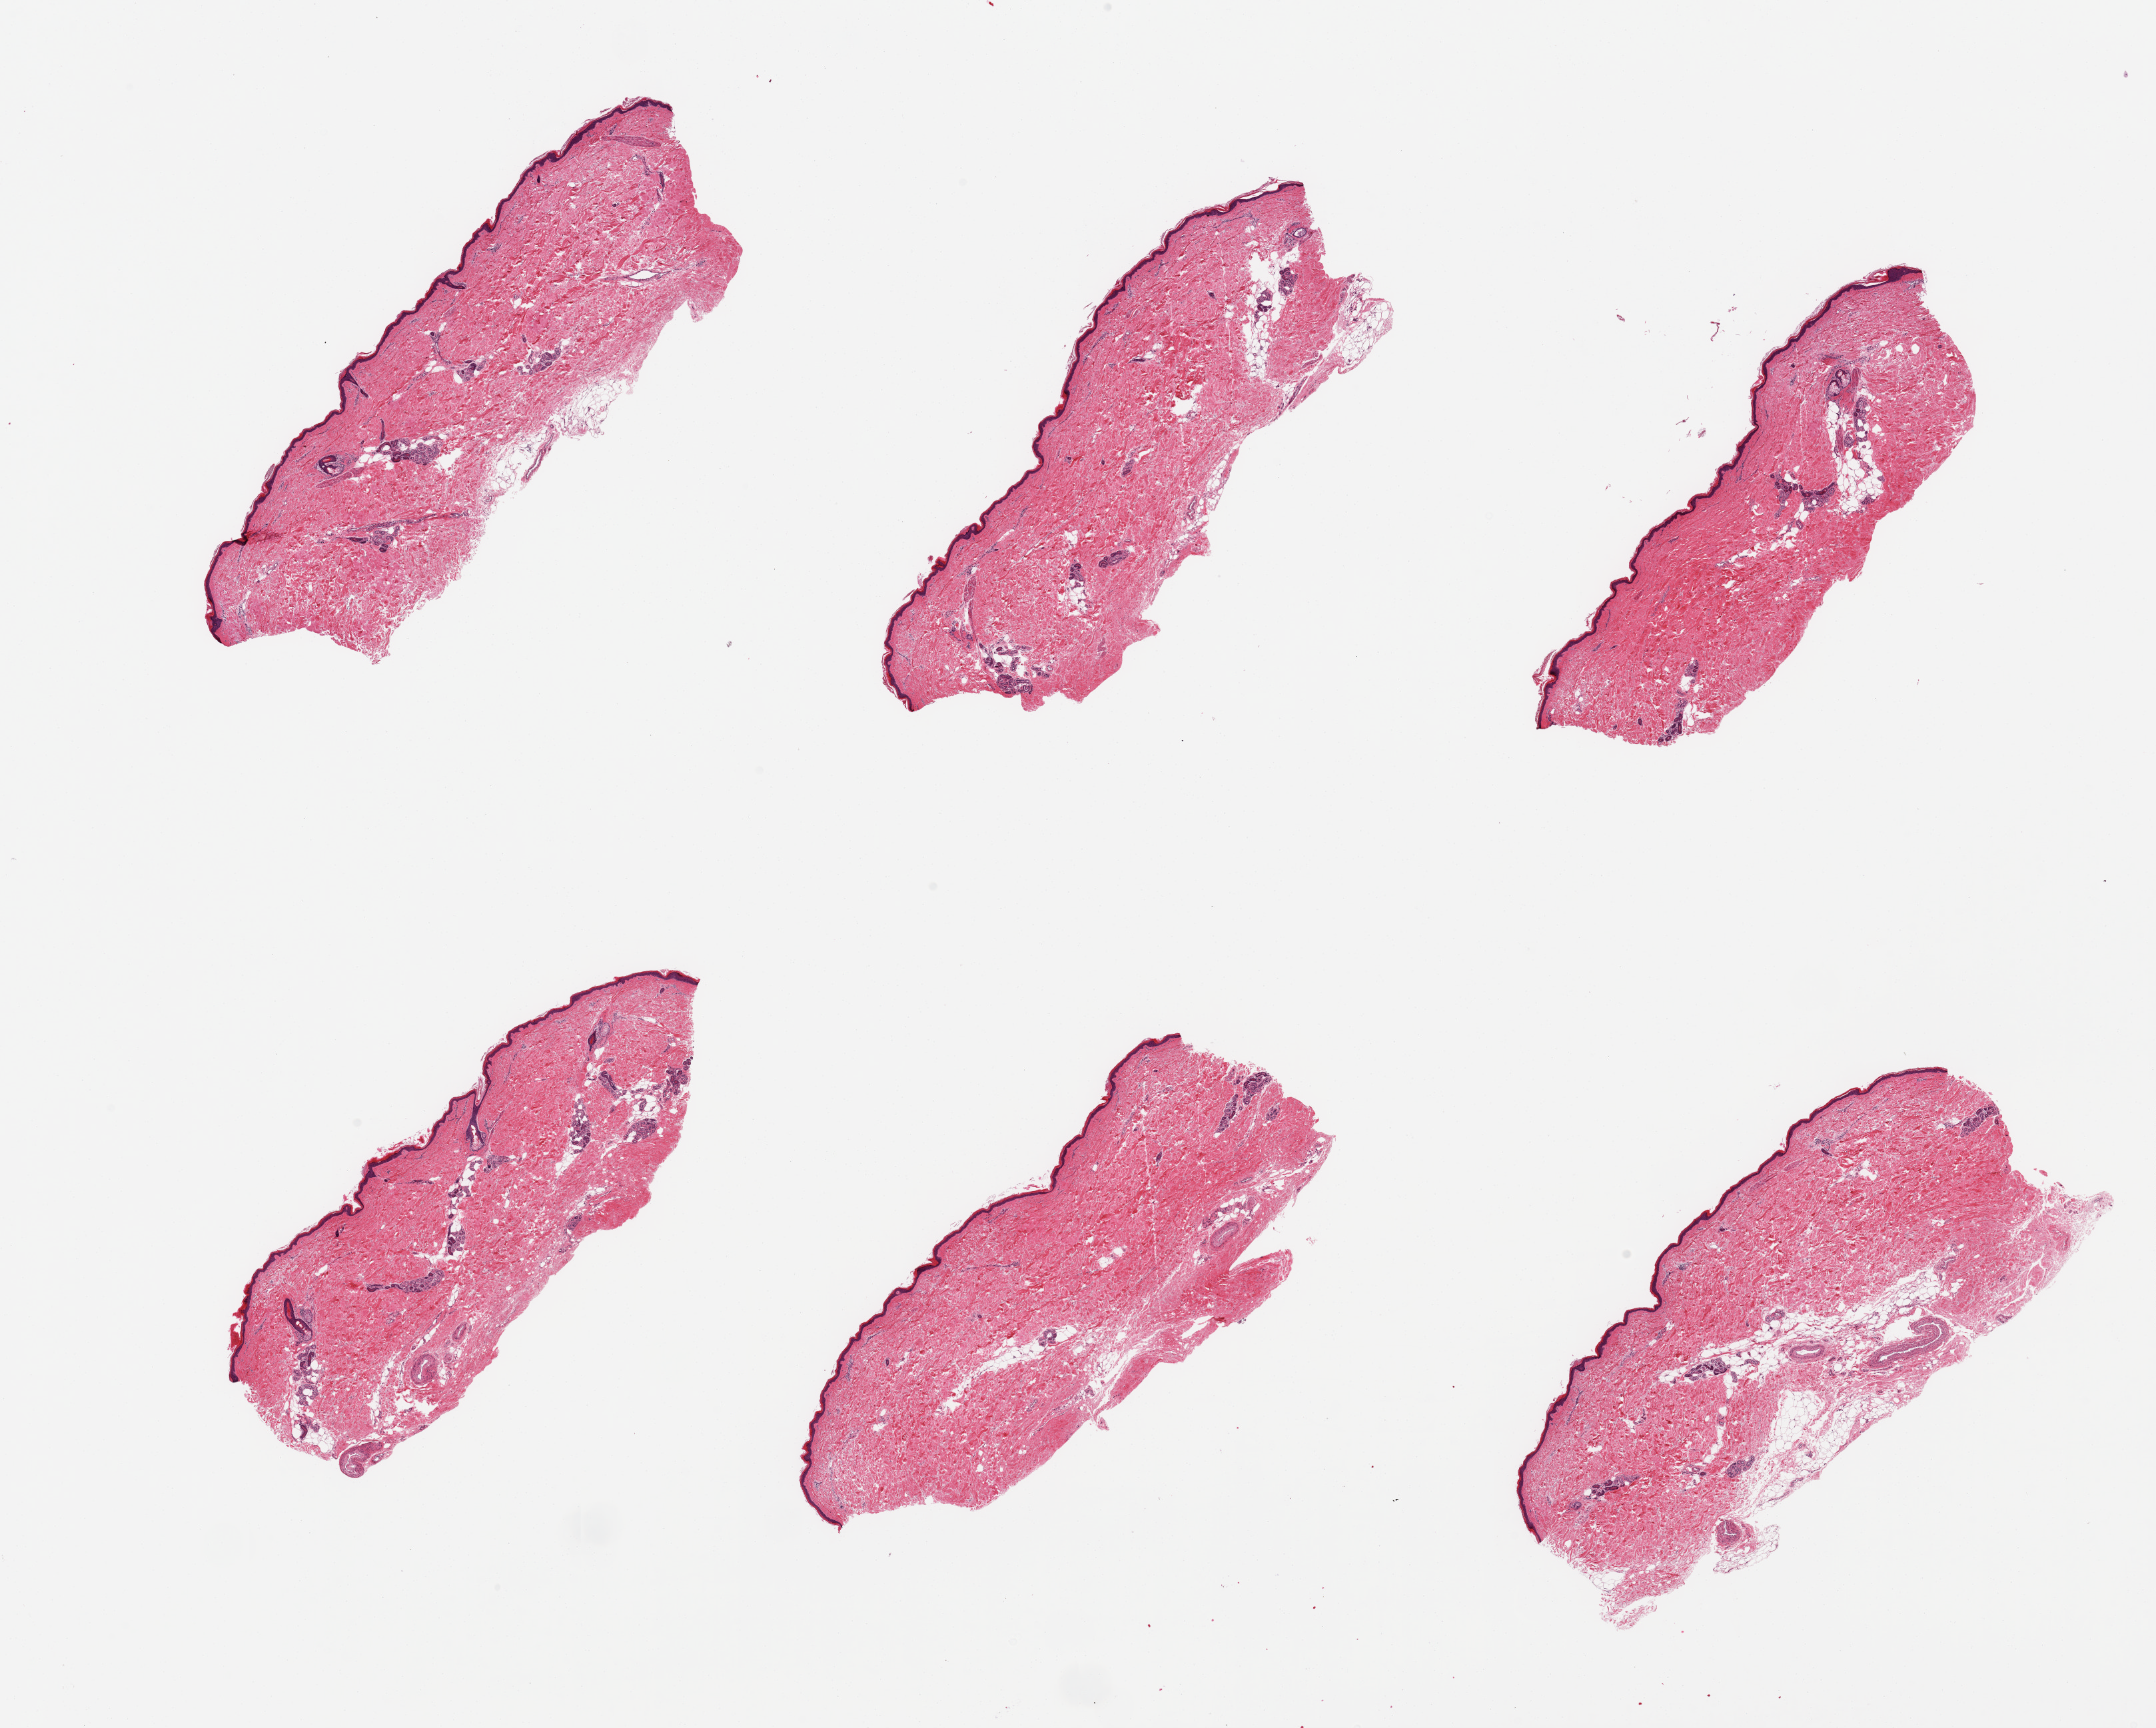
Digitized haematoxylin and eosin-stained section, a low-resolution overview of the entire scanned area, about 25.6 x 20.5 mm (acquisition: 20x scan); PAXgene-fixed paraffin-embedded (PFPE) section; target tissue: skin of lower leg; donor tissue sample.
- review note (as recorded): 6 pieces, squamous epithelium is ~30-40 microns